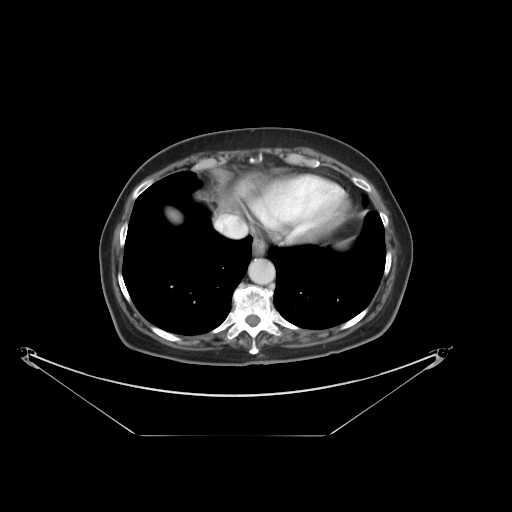
Contrast-enhanced abdominal CT, one axial slice; slice 33 of 36 in the series (ordered by position); 120 kVp; intravenous contrast given; soft-tissue window (W 400 / L 40 HU); 512 × 512 image matrix, field of view 500 × 500 mm. Female patient, age 70 years. Case-level facts recorded for this patient, not image findings: diagnosis: colorectal cancer liver metastases, imaged before liver resection; multiple liver metastases: no; largest metastasis: 2.5 cm; chemotherapy before resection: no.
Structures marked on this image (manually delineated by an expert):
- hepatic veins: bounding box <216,215,237,237> (left, top, right, bottom; pixels)